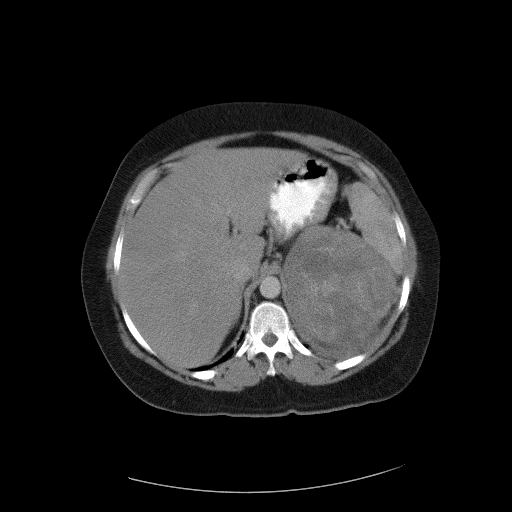
Contrast-enhanced abdominal CT, one axial slice; position 75 of 90 along the scan axis; intravenous contrast given; soft-tissue window (W 400 / L 40 HU); 5 mm slice thickness; 512 × 512 image matrix, field of view 480 × 480 mm. Female patient, age 55 years. From the clinical record (not read from this slice): diagnosis: adrenocortical carcinoma; tumour side: left adrenal; tumour size at pathology: 22 cm; Ki-67 index: 10 %; stage (as recorded): 3.
Outlined on this slice (semi-automatically segmented with operator editing):
- mass: box from (x=287, y=229) to (x=393, y=343) px